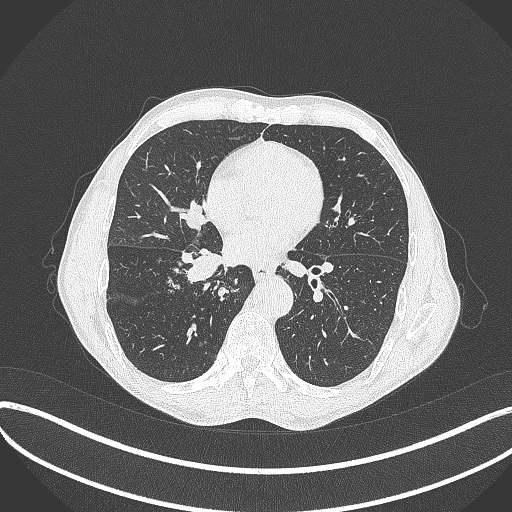
Chest CT, one axial slice. Position 193 of 481 along the scan axis. Reconstruction kernel B70f. 120 kVp. Lung window (W 1500 / L -600 HU). 1 mm slice thickness. 512 × 512 image matrix, field of view 400 × 400 mm. Patient: male, 65 years. Case-level facts recorded for this patient, not image findings: clinical TNM (as recorded): T2a N0 M0.
Annotated regions visible in this slice (bounding box drawn by a radiologist):
- lung tumour (recorded histology: squamous cell carcinoma): bounding box [x1, y1, x2, y2] px = [175, 246, 226, 287]